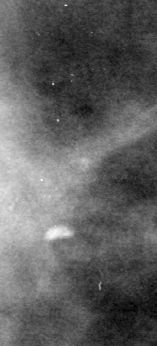
Crop from a digitized film mammogram around one marked abnormality; left breast; CC view; BI-RADS breast density category 3 (scale 1–4).
- Finding: calcifications, morphology pleomorphic, distribution clustered; BI-RADS assessment category 4; pathology result (as recorded, not read from the image): malignant.